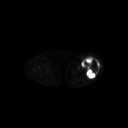
FDG PET of an extremity soft-tissue mass (from a PET/CT study), one axial slice. 128 × 128 image matrix. Female patient, age 62 years. From the clinical record (not read from this slice): histological type: undifferentiated – high grade; grade: high; site of the primary tumour: left thigh.
Structures marked on this image (expert contour drawn on MRI and transferred to this co-registered scan by the dataset authors):
- gross tumour volume including surrounding oedema: bounding box <81,56,100,78> (left, top, right, bottom; pixels)
- gross tumour volume (mass): <81,56,100,78>